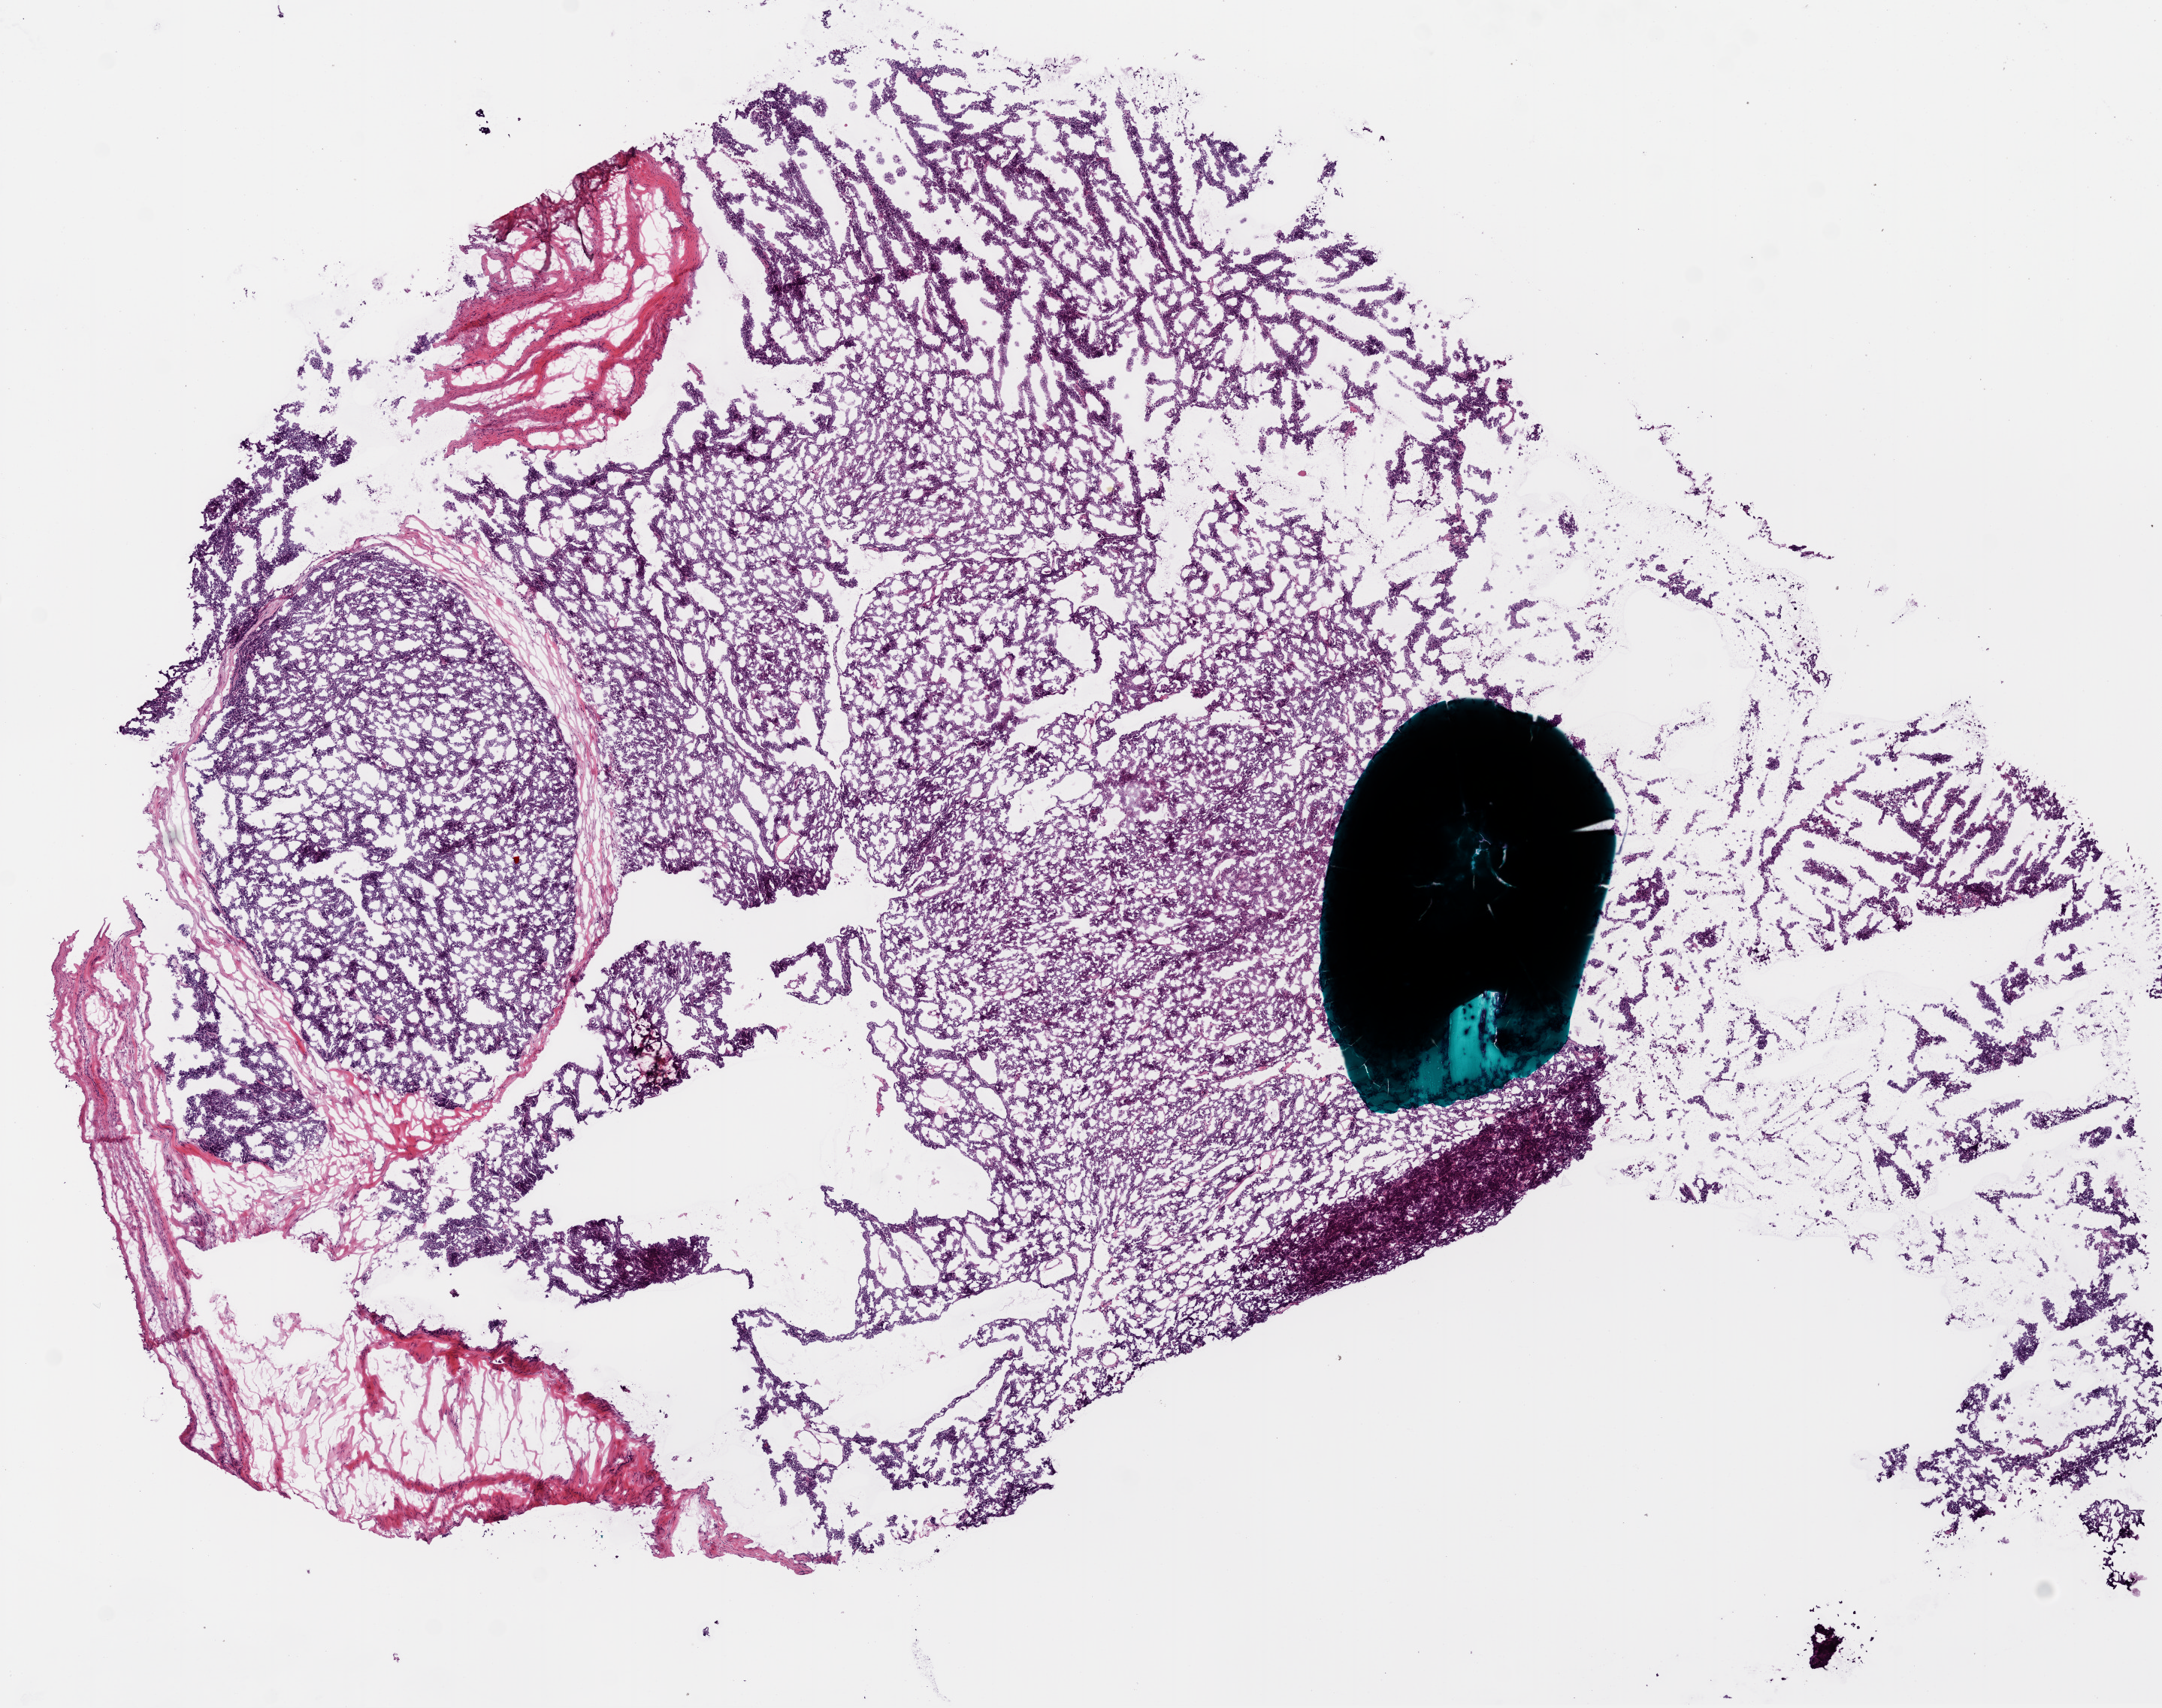
Whole-slide histology image, H&E-stained — a low-resolution overview of the entire scanned area, about 11.6 x 9.2 mm (slide scanned at 20x); frozen section from the bottom of the tissue portion; ovary, primary tumour sample. Patient: female, age at initial diagnosis 55 years. Histologic grade: G3 (poorly differentiated). Composition of this section per pathologist review: tumour cells 83%, tumour nuclei 91%, normal cells 17%, stromal cells 0%, necrosis 0%.
- diagnosis: Serous cystadenocarcinoma, NOS
- FIGO stage: IIIB